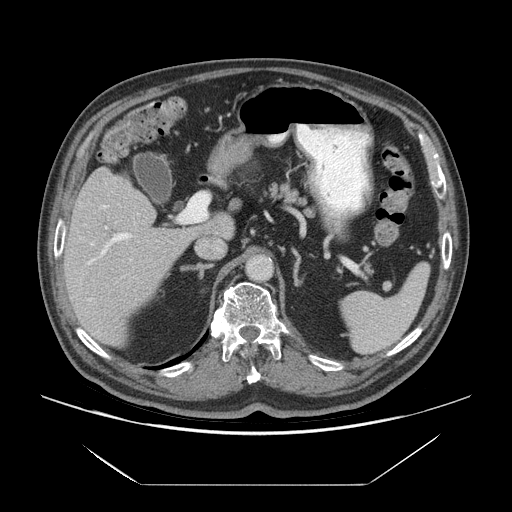
Contrast-enhanced abdominal CT (liver protocol), one axial slice. Slice 38 of 75 in the series (ordered by position). Reconstruction kernel STANDARD. 140 kVp. Soft-tissue window (W 400 / L 40 HU). 2.5 mm slice thickness. 512 × 512 image matrix, field of view 420 × 420 mm. From the clinical record (not read from this slice): diagnosis: hepatocellular carcinoma (patient treated with transarterial chemoembolisation; whether this scan precedes or follows treatment is not stated here); TNM stage (as recorded): Stage-I.
Structures marked on this image (semi-automatic segmentation, software-assisted and operator-edited):
- liver parenchyma outside the tumour (the mass and vessels are separate outlines, so this box may not span the whole liver): box from (x=64, y=166) to (x=198, y=346) px
- liver vessels: (x=80, y=205)–(x=132, y=302)